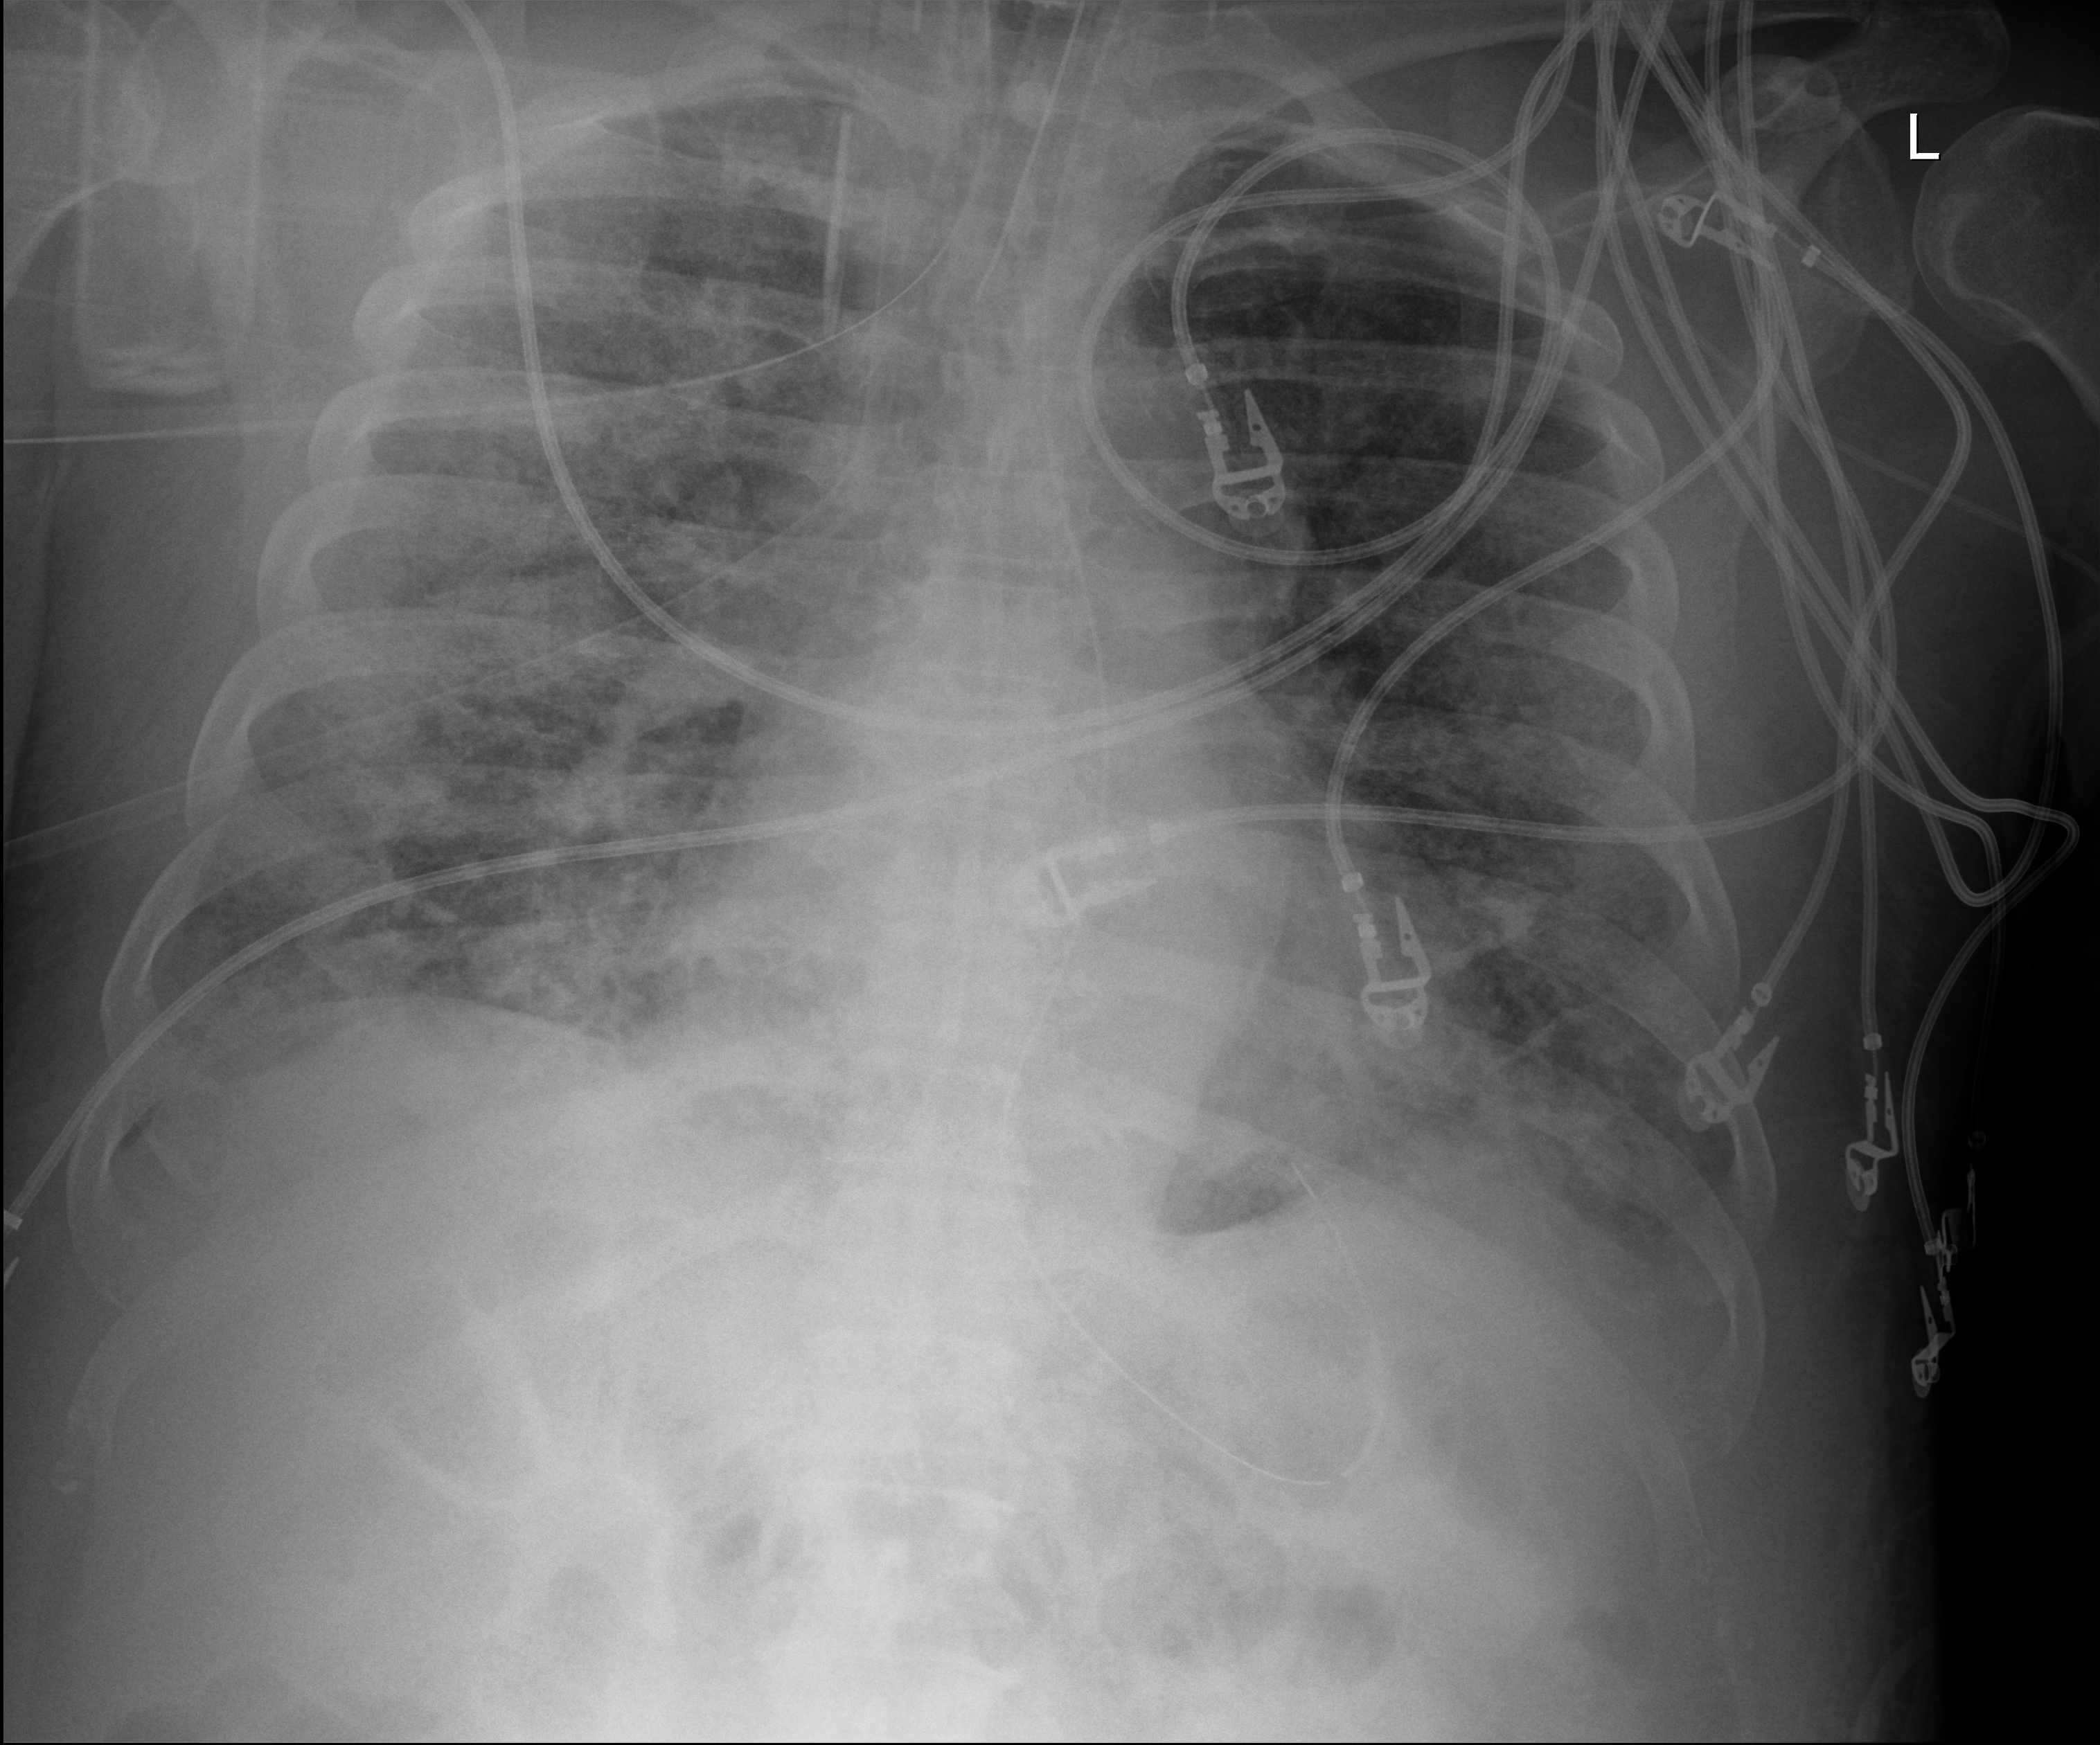
Chest X-ray (portable); anteroposterior (AP) projection. Male patient hospitalised with COVID-19, age 60–74 years.
Admission-level facts for this patient (not findings on this image; timing relative to this image not recorded): hypertension (admission record): yes; mechanically ventilated during this hospital stay: yes.